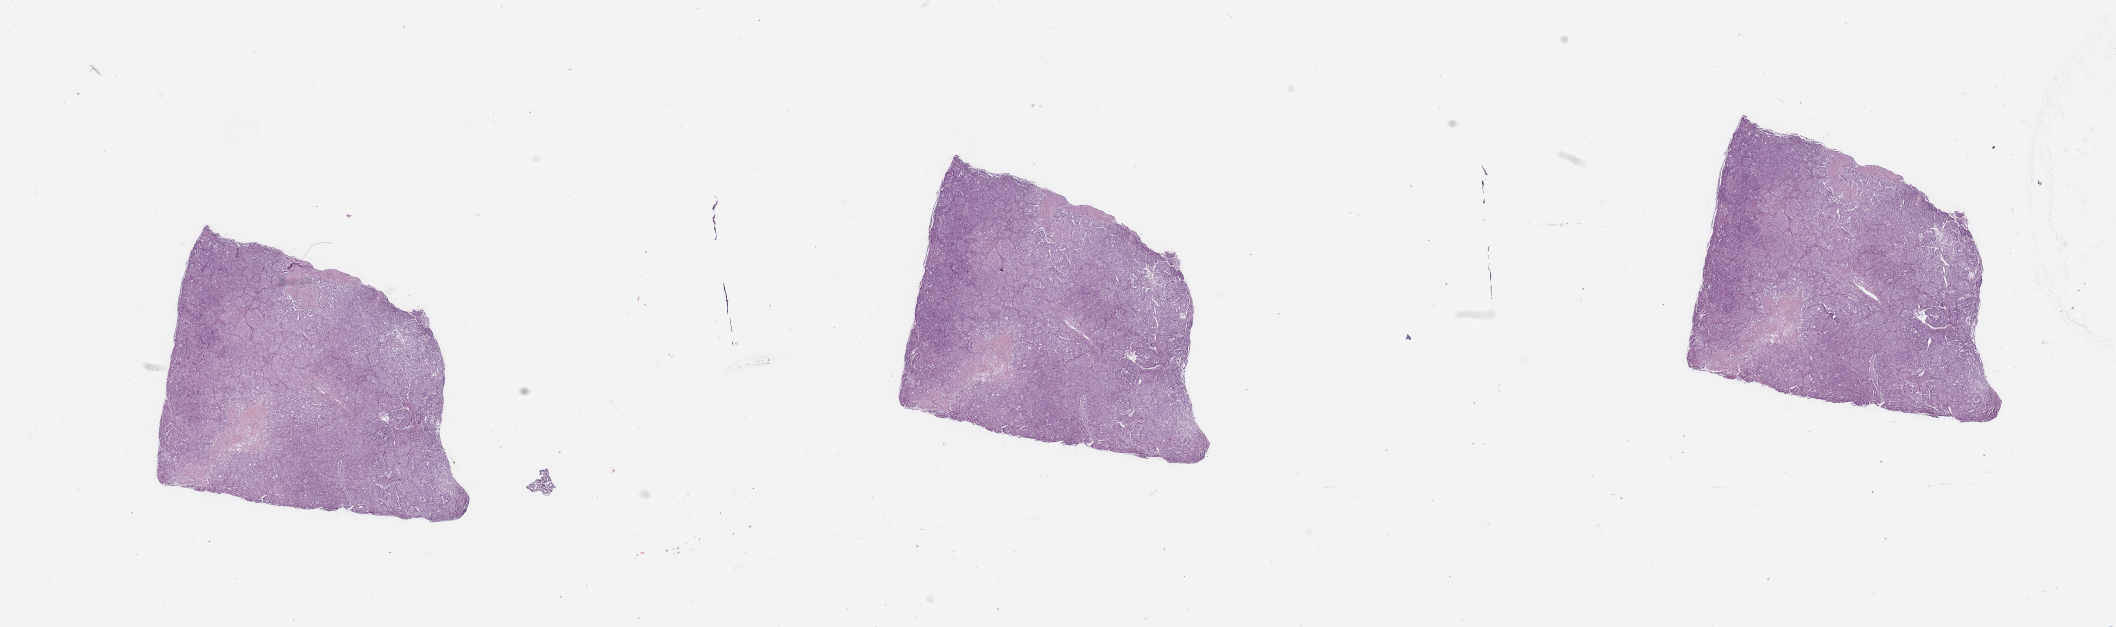
Digitized Hematoxylin and eosin (H&E) stained tissue section (whole slide), whole scanned area (about 33.5 x 9.9 mm, acquisition: 20x scan) shown as a low-resolution overview; tumour tissue sample, sampled site: lung. Male, 51 y/o. Histologic grade: G2 (moderately differentiated). Composition of this section per pathologist review: tumour nuclei 80%, necrosis 10%.
AJCC pathologic stage: IIIA. Histologic diagnosis: Adenocarcinoma, NOS.